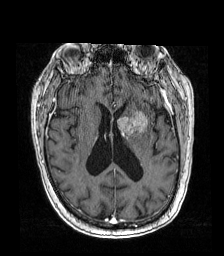
Brain MRI from a brain-tumour surgery series, one axial slice. Position 77 of 192 along the scan axis. T1-weighted post-contrast. 224 × 256 image matrix, field of view 219 × 250 mm. From the clinical record (not read from this slice): histopathology: Metastatic carcinoma from lung primary.
Annotated regions visible in this slice (manually delineated by an expert):
- tumour: bounding box <117,110,148,145> (left, top, right, bottom; pixels)